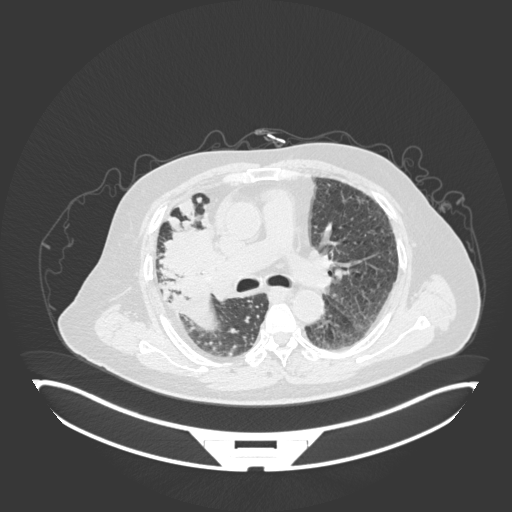
Chest CT, one axial slice; position 102 of 201 along the scan axis; reconstruction kernel B30f; lung window (W 1500 / L -600 HU); 1 mm slice thickness; 512 × 512 image matrix, field of view 500 × 500 mm. Male patient, age 69 years. From the clinical record (not read from this slice): clinical TNM (as recorded): T4 N3 M1.
Structures marked on this image (rectangle marked by the reading radiologist):
- lung tumour (recorded histology: adenocarcinoma): bounding box <158,223,215,282> (left, top, right, bottom; pixels)